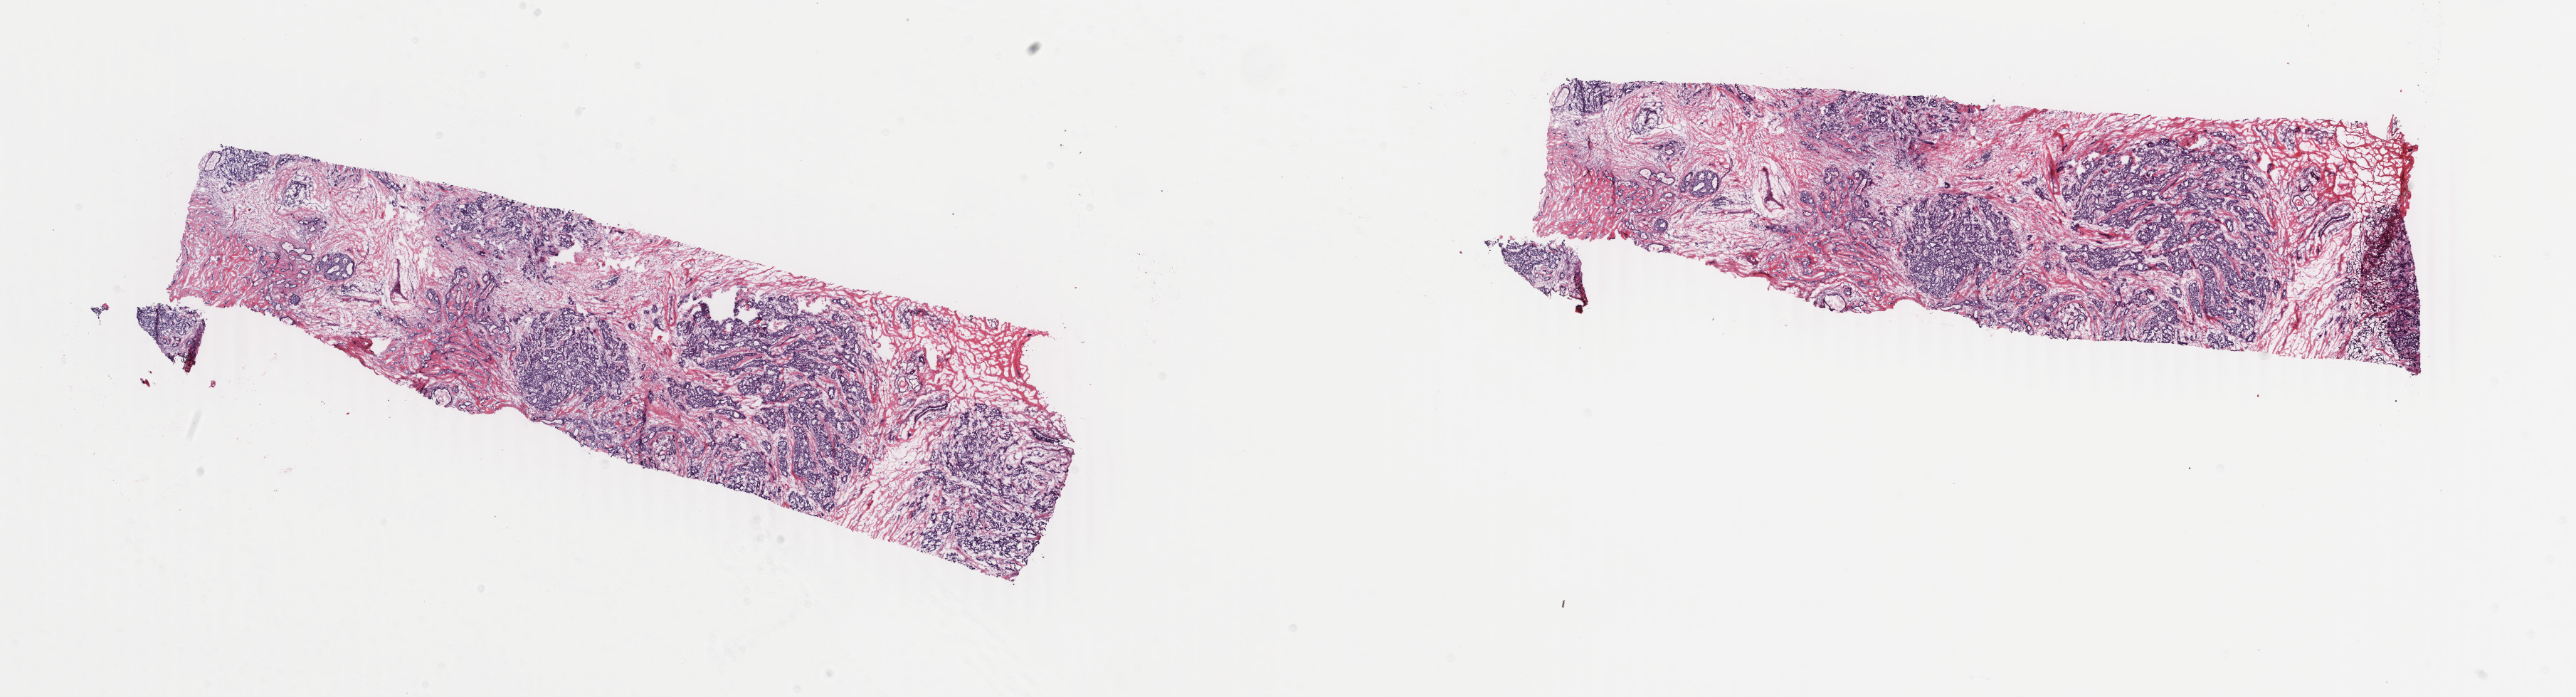
Digitized H&E-stained tissue section (whole slide) — a low-resolution overview of the entire scanned area, about 28.8 x 7.8 mm (slide scanned at 40x). Frozen section. Sample: primary tumour, breast. Patient: female, age at initial diagnosis 39 years. Slide review estimates, as recorded: tumour cells 70%, tumour nuclei 70%, normal cells 0%, stromal cells 30%, necrosis 0%. Infiltration values recorded for this section: lymphocyte infiltration 30%, monocyte infiltration 10%, neutrophil infiltration 20%.
• lymph nodes positive (case pathology): 0 of 4 examined
• pathologic diagnosis: Infiltrating duct carcinoma, NOS
• AJCC pathologic stage: IIA